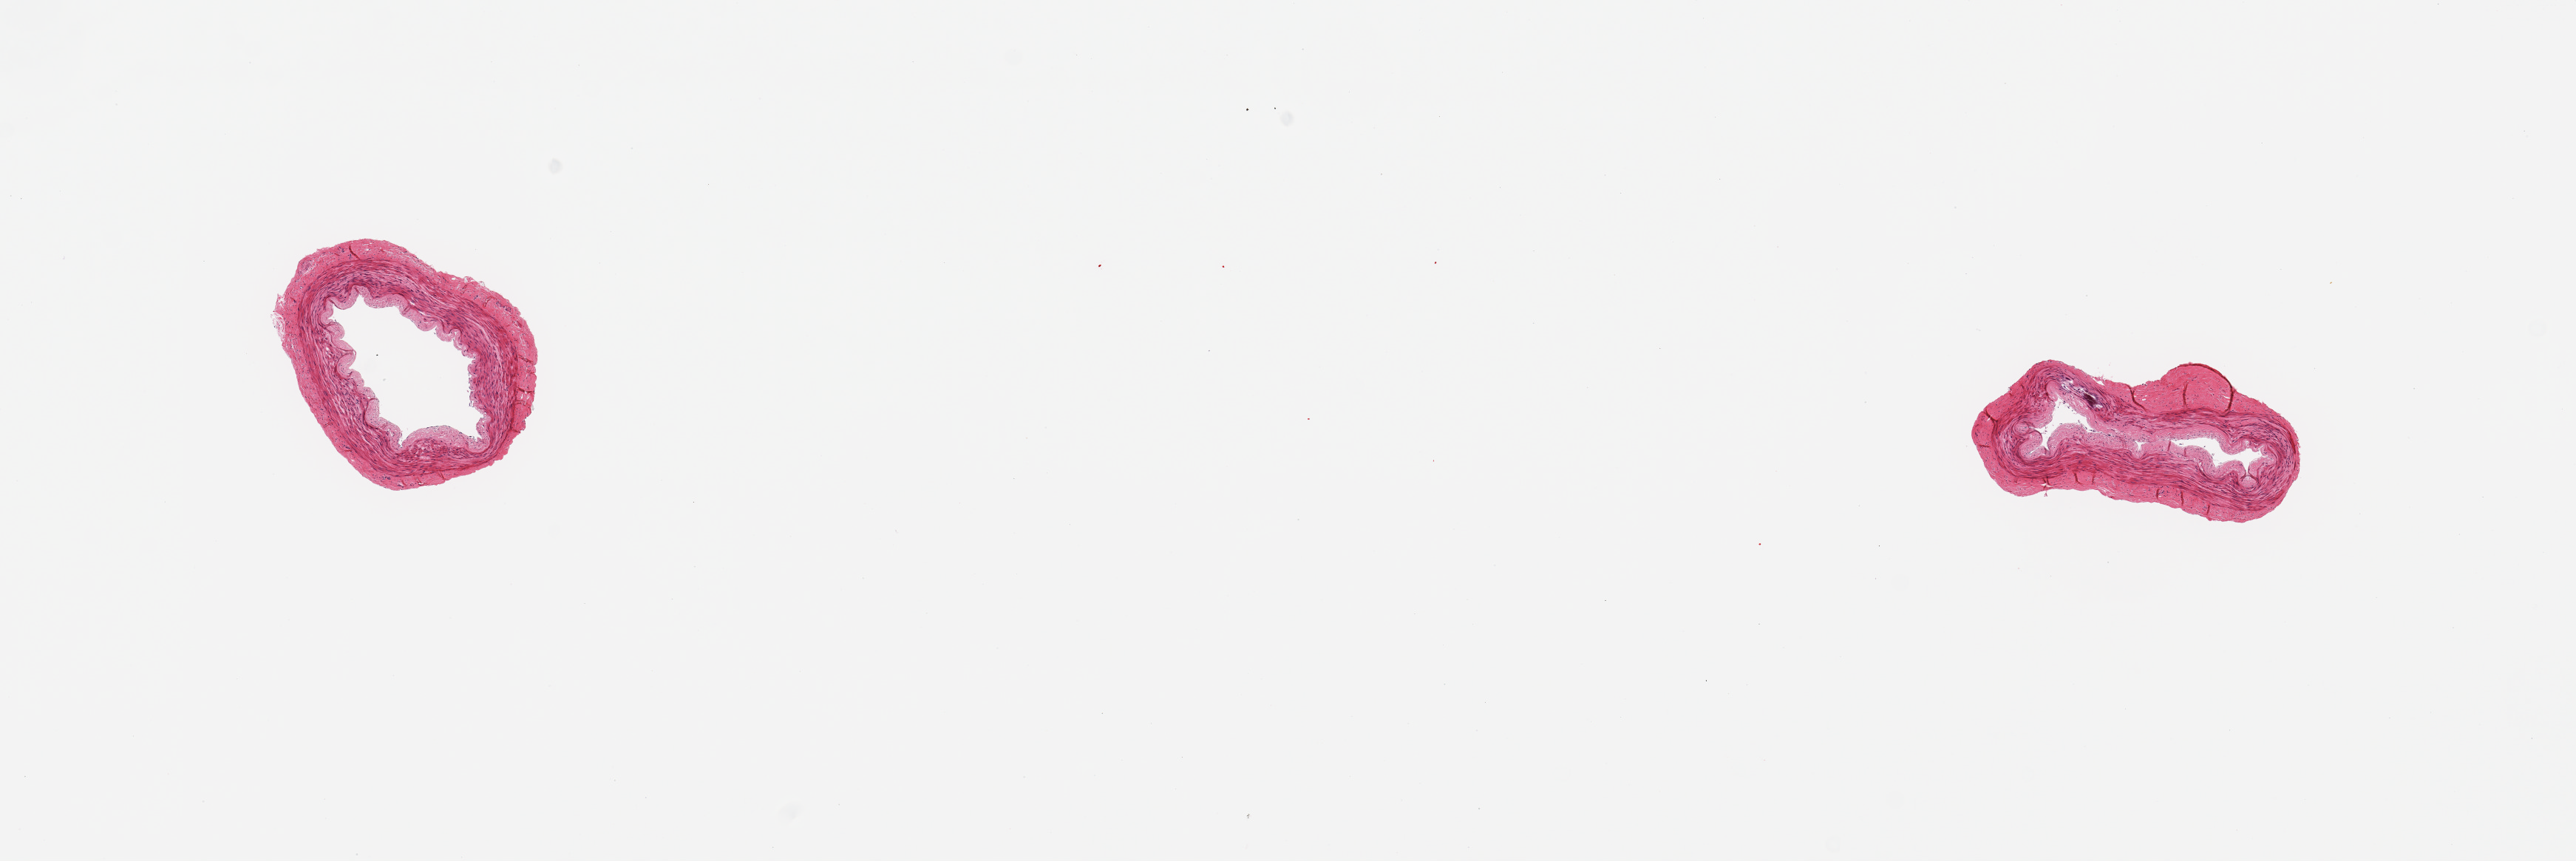
Whole-slide image, hematoxylin and eosin (H&E) stain, shown as a low-resolution overview of the whole scanned area (about 13.8 x 4.6 mm, acquisition: 20x scan); PAXgene-fixed, paraffin-embedded tissue; target tissue: tibial artery; tissue donor sample. Donor: female.
Pathologist's review note for this sample: 2 pieces: focal medial calcification in 1; mild fibrous intimal thickening.